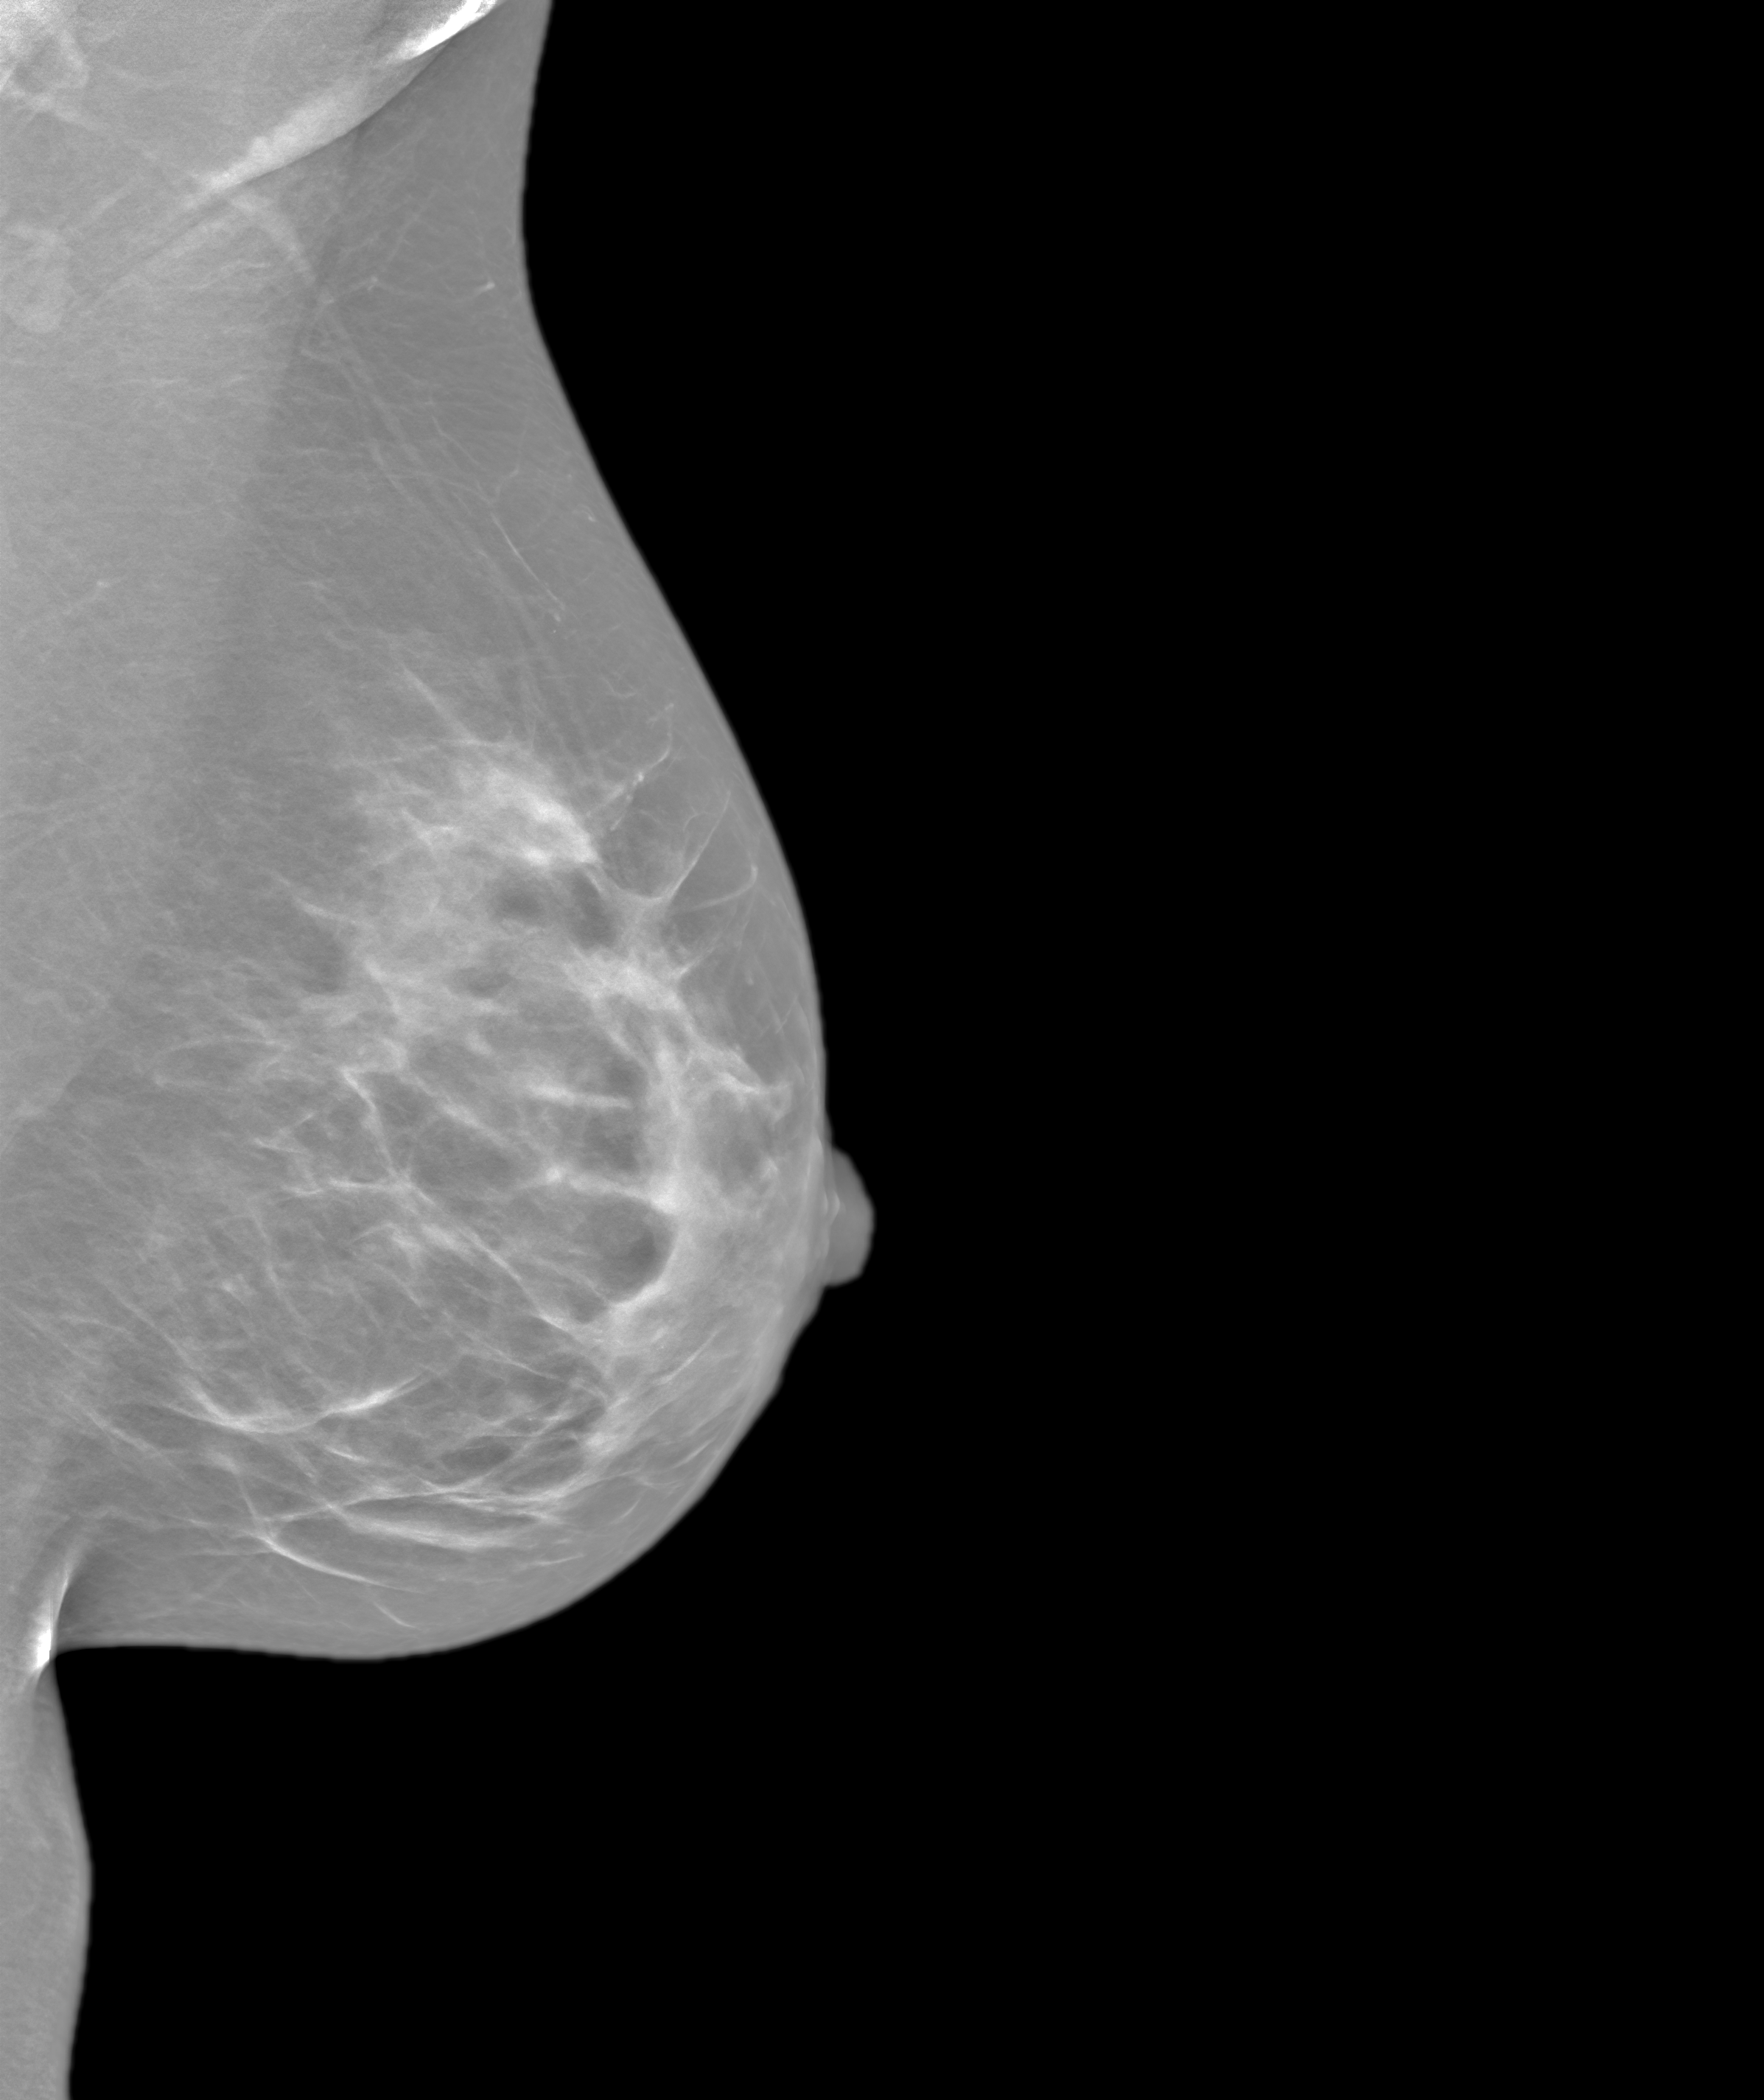
Screening examination. Patient: female, 47 years.
Image type: synthesized 2-D view from tomosynthesis. Breast: left. Projection: medio-lateral oblique projection.